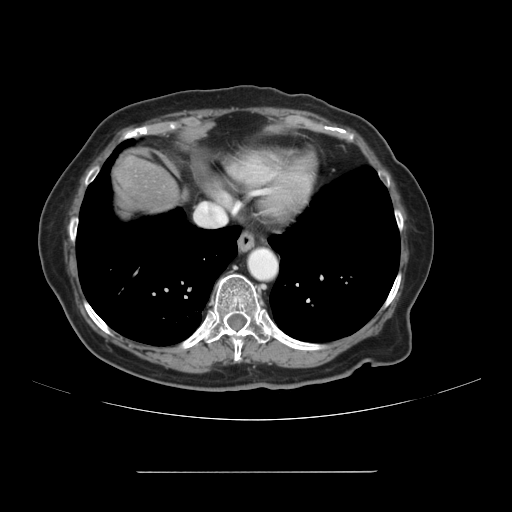
Contrast-enhanced abdominal CT, one axial slice. 120 kVp. Intravenous contrast given. Soft-tissue window (W 400 / L 40 HU). 2.5 mm slice thickness. 512 × 512 image matrix, field of view 400 × 400 mm. Female patient, age 74 years. Case-level facts recorded for this patient, not image findings: diagnosis: colorectal cancer liver metastases, imaged before liver resection; multiple liver metastases: yes; largest metastasis: 1.1 cm; disease in both lobes: yes.
Outlined on this slice (expert manual segmentation):
- liver: box from (x=111, y=154) to (x=179, y=215) px